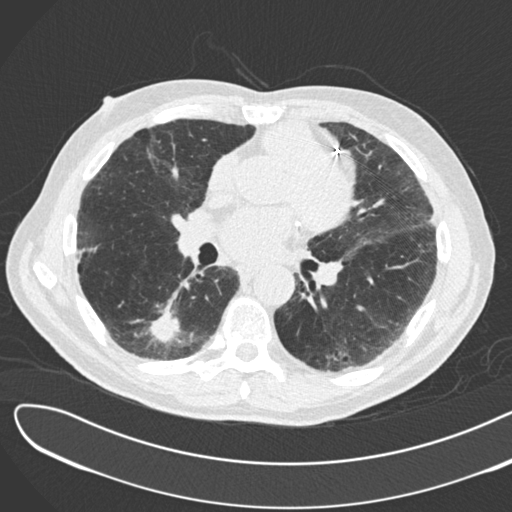
Low-dose screening chest CT, axial slice; second annual screen; lung window (W 1500 / L -600 HU); 2 mm slice thickness; slice 97 of 183 in the series. Male participant, aged 72 years at enrolment. Former smoker at enrolment.
Expert-annotated lung lesion, bounding box (x1, y1, x2, y2) in pixels: (130, 290, 195, 352). The screening reader recorded 2 non-calcified nodules or masses ≥4 mm on this exam; which of them this box marks is not recorded. Participant outcome: lung cancer diagnosed 46 days after this screen — squamous cell carcinoma, NOS, right lower lobe, poorly differentiated (G3), stage IB (AJCC 6th edition), 42 mm at pathology.